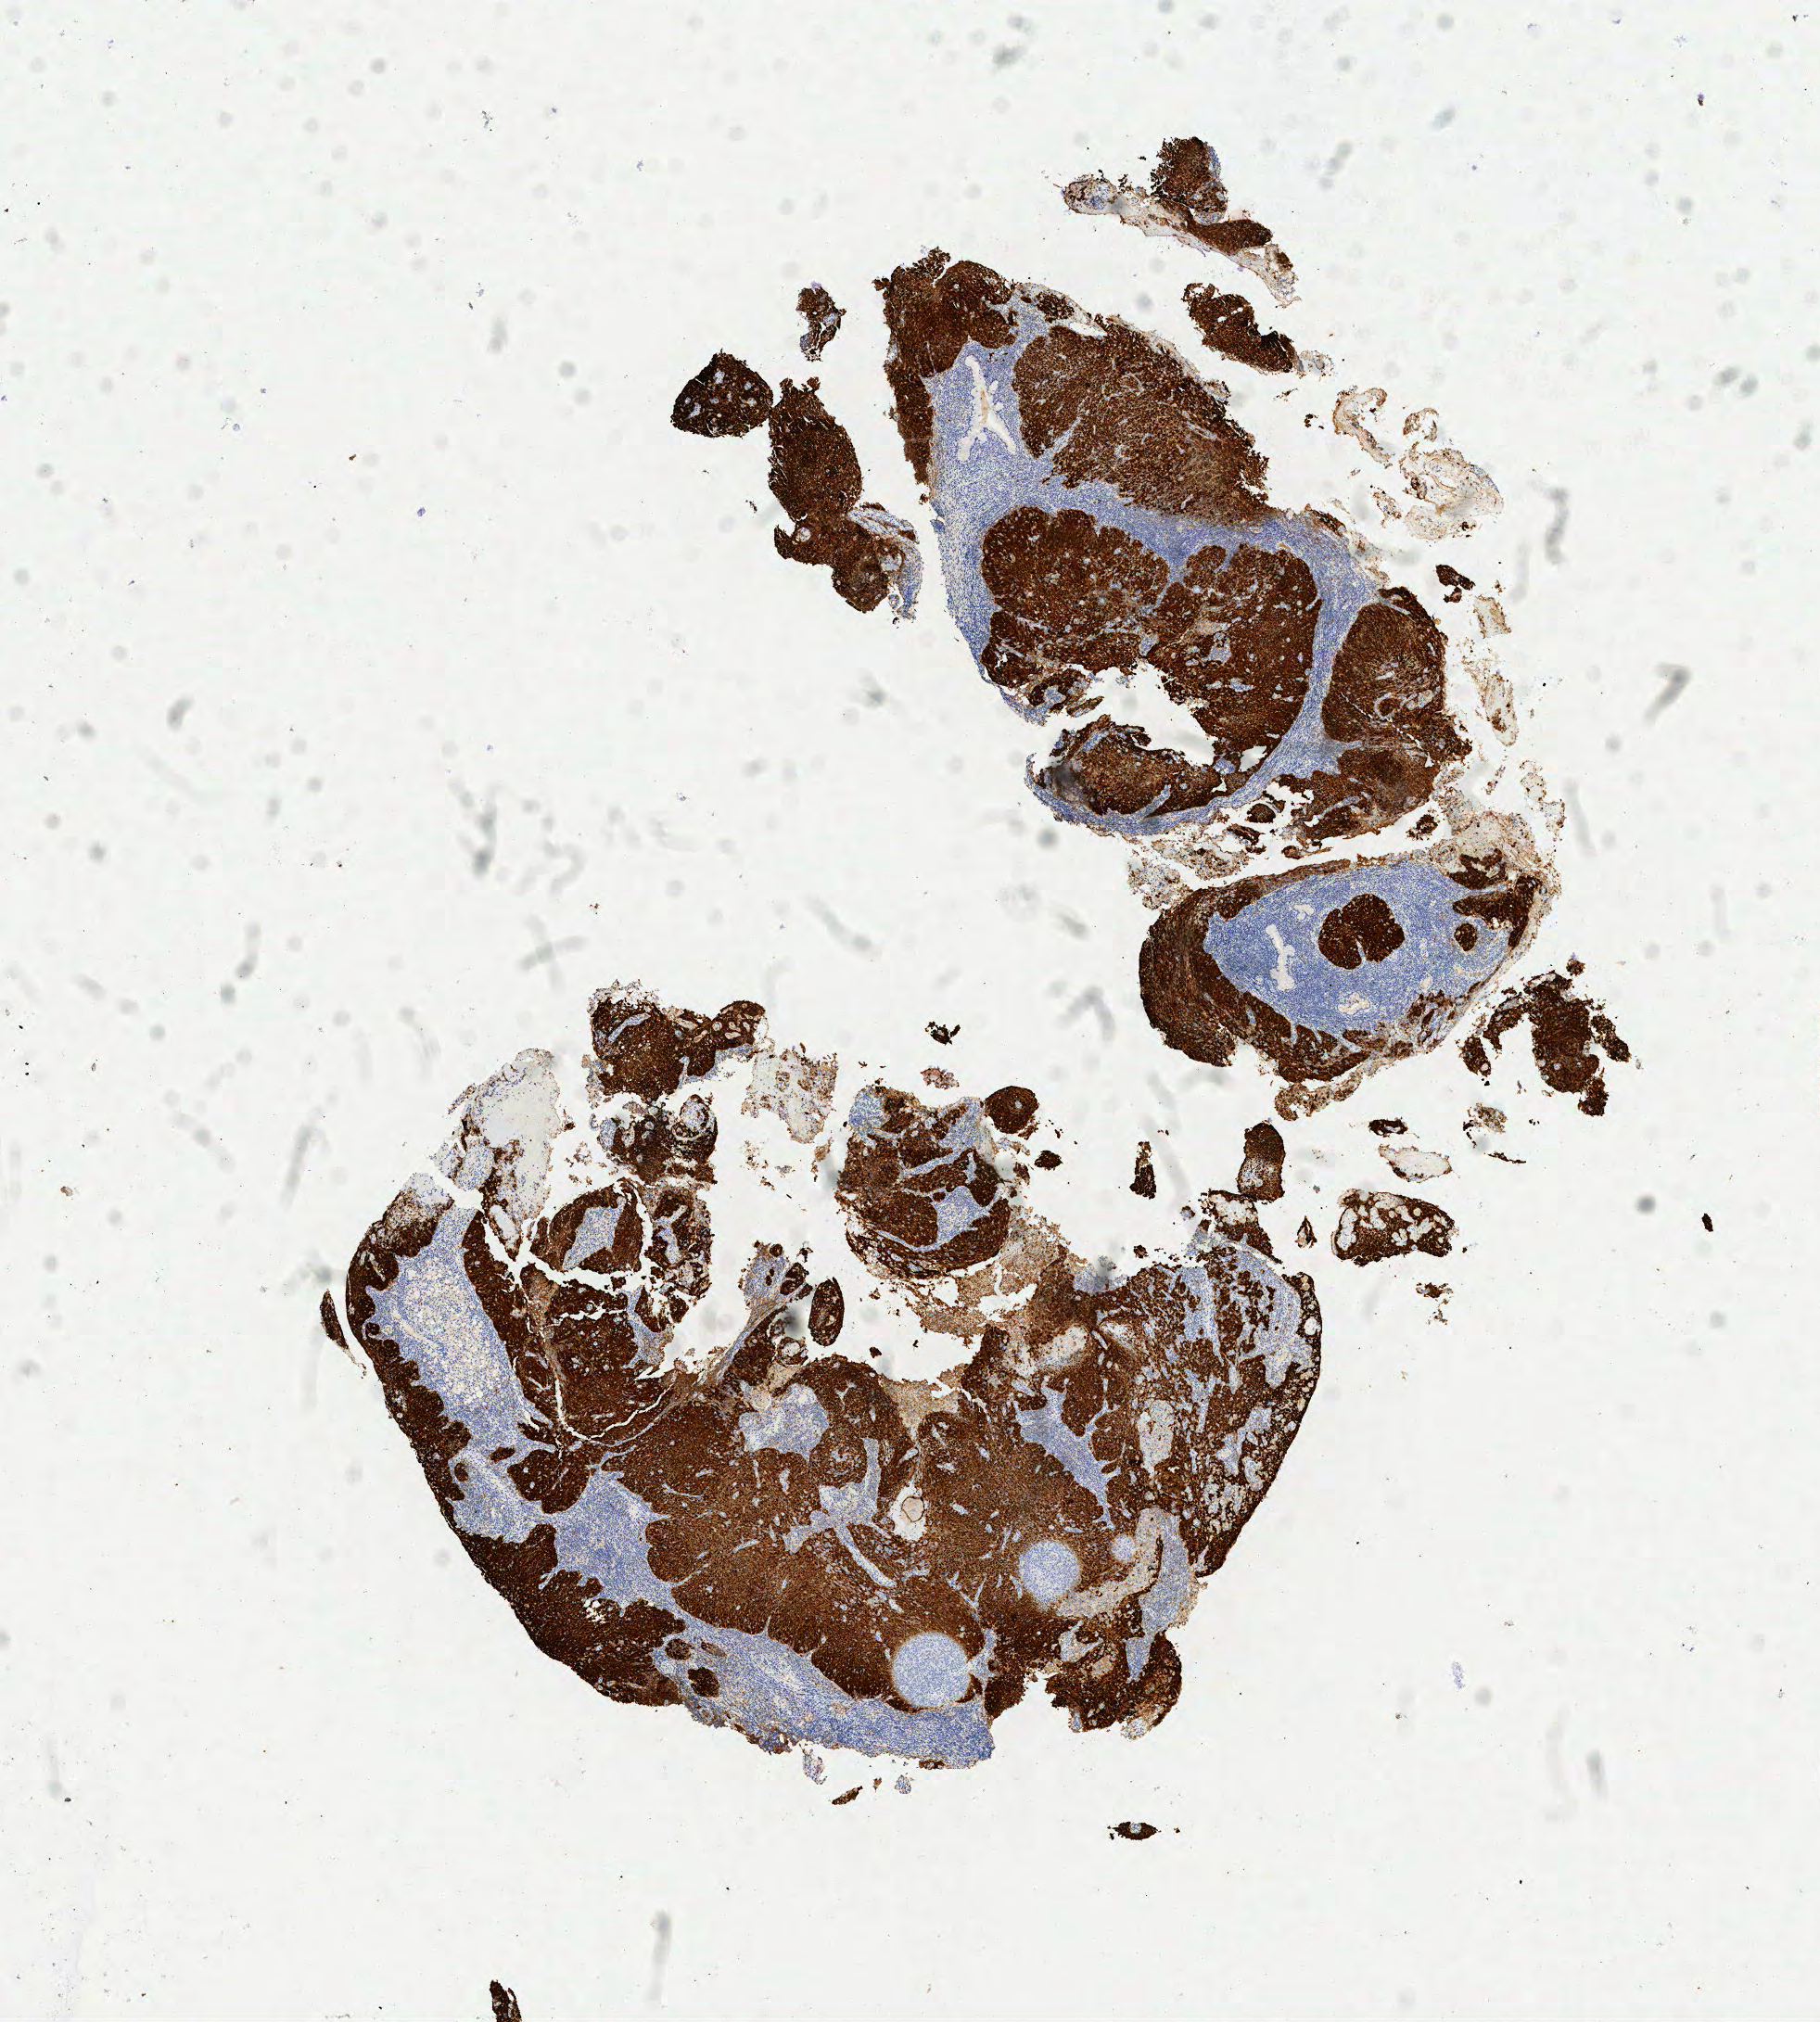
IHC for p16 (p16INK4a), whole-slide image — whole scanned area (about 7.8 x 8.7 mm) shown as a low-resolution overview, tumor tissue, site: cervix. Female patient, aged 62.
Diagnosis: Squamous cell carcinoma, large cell, nonkeratinizing, NOS.